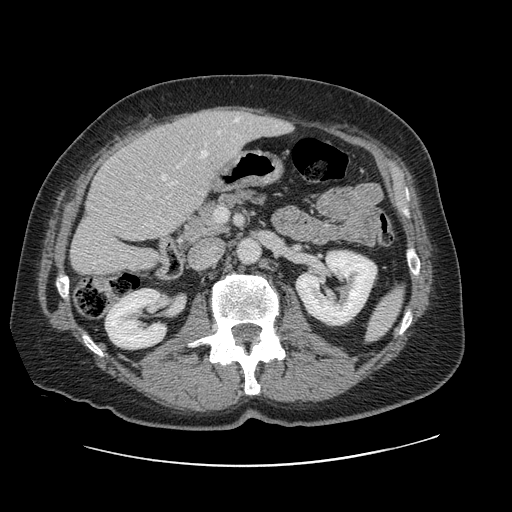
Contrast-enhanced abdominal CT, one axial slice; slice 40 of 138 in the series (ordered by position); 120 kVp; intravenous contrast given; soft-tissue window (W 400 / L 40 HU); 2.5 mm slice thickness; 512 × 512 image matrix, field of view 402 × 402 mm. Male patient, age 71 years. From the clinical record (not read from this slice): diagnosis: colorectal cancer liver metastases, imaged before liver resection; multiple liver metastases: no; largest metastasis: 3.3 cm; disease in both lobes: no.
Structures marked on this image (manually delineated by an expert):
- hepatic veins: box from (x=171, y=118) to (x=239, y=185) px
- liver: (x=72, y=108)–(x=289, y=275)
- planned liver remnant (the part of the liver to remain after resection): (x=72, y=134)–(x=191, y=276)
- portal vein (with intrahepatic branches): (x=162, y=176)–(x=166, y=180)